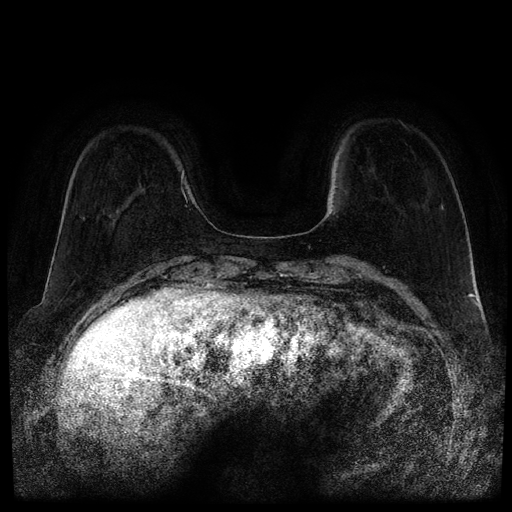
Breast MRI (dynamic contrast-enhanced, multi-phase), one axial slice; position 30 of 116 along the scan axis; dynamic contrast-enhanced series, time point 2 of 5 at this slice position (early post-contrast); 1.5 T; TE 2.6 ms, TR 5.3 ms; 2.1 mm slice thickness; 512 × 512 image matrix, field of view 350 × 350 mm. Patient: female, 66 years.
Structures marked on this image (semi-automatically segmented with operator editing):
- breast lesion (labelled benign in the annotation): bounding box (x1, y1, x2, y2) in pixels: (108, 215, 112, 218)